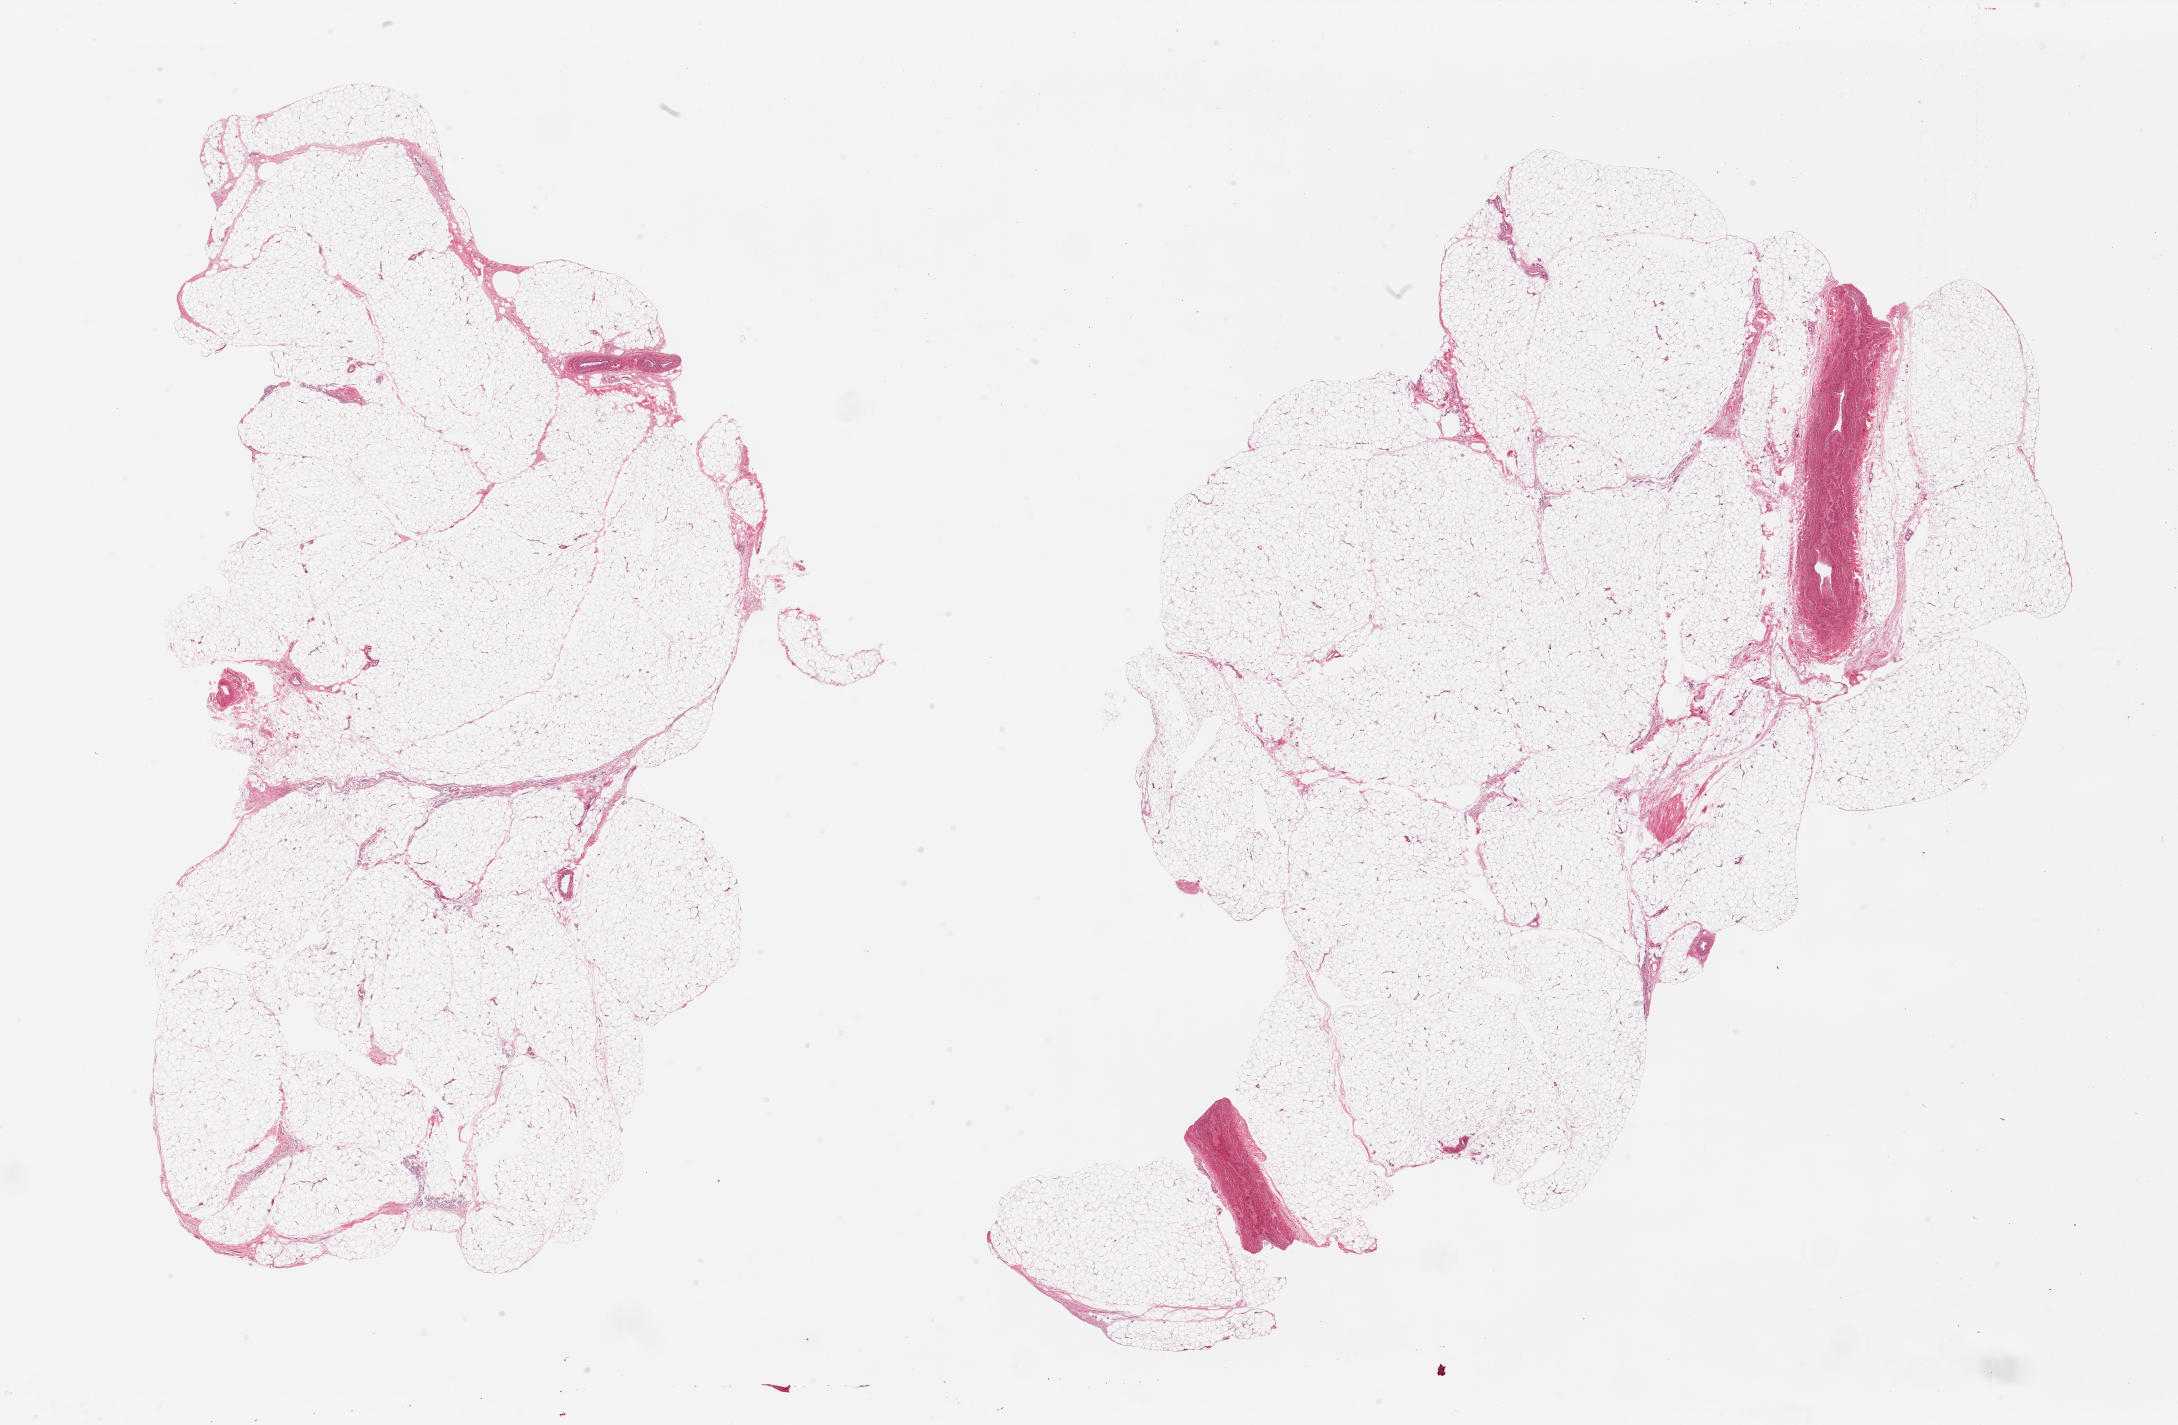
Whole-slide image, H&E stain, brightfield — low-resolution overview of the scanned area, about 34.5 x 22.5 mm; PAXgene-fixed, paraffin-embedded tissue; sampled site (target tissue): adipose tissue; tissue donor sample. Donor: male.
Reviewer comment on this tissue sample: 2 pieces, ~10% fascia/vascular tissue.